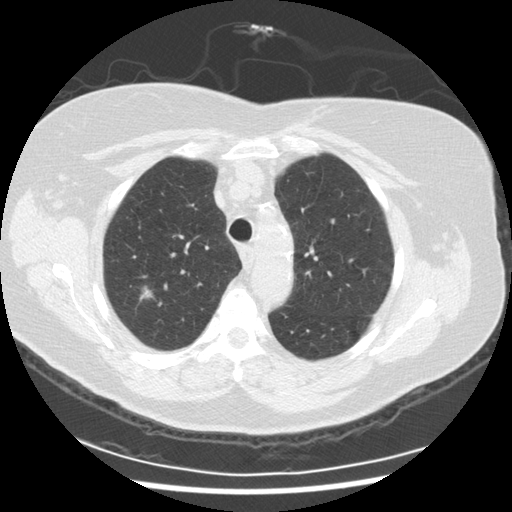
Low-dose screening chest CT, axial slice, third annual screen, lung window (W 1500 / L -600 HU), 2.5 mm slice thickness, standard (soft-tissue) reconstruction kernel (STANDARD). Female, age 72 years at enrolment. Current smoker at enrolment.
Expert reader's lesion annotation, bounding box [x1, y1, x2, y2] px = [129, 280, 161, 309]. Screening reader's record for this exam (one nodule recorded; not confirmed to be the boxed lesion): non-calcified nodule or mass ≥4 mm, right upper lobe, 9 × 8 mm, poorly defined margins, ground glass attenuation, pre-existing on the prior screen: no. Participant outcome: lung cancer diagnosed 121 days after this screen — squamous cell carcinoma, NOS, right upper lobe, poorly differentiated (G3), stage IIIA (AJCC 6th edition), 22 mm at pathology.